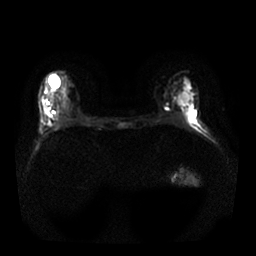
Breast MRI, one axial slice. Position 11 of 25 along the scan axis. Diffusion-weighted series; image 2 of 4 stored at this slice position (different b-values; order by instance number). 1.5 T. 256 × 256 image matrix, field of view 340 × 340 mm. Female patient.
Outlined on this slice (expert manual segmentation):
- tumour on diffusion-weighted imaging: box from (x=59, y=106) to (x=67, y=120) px